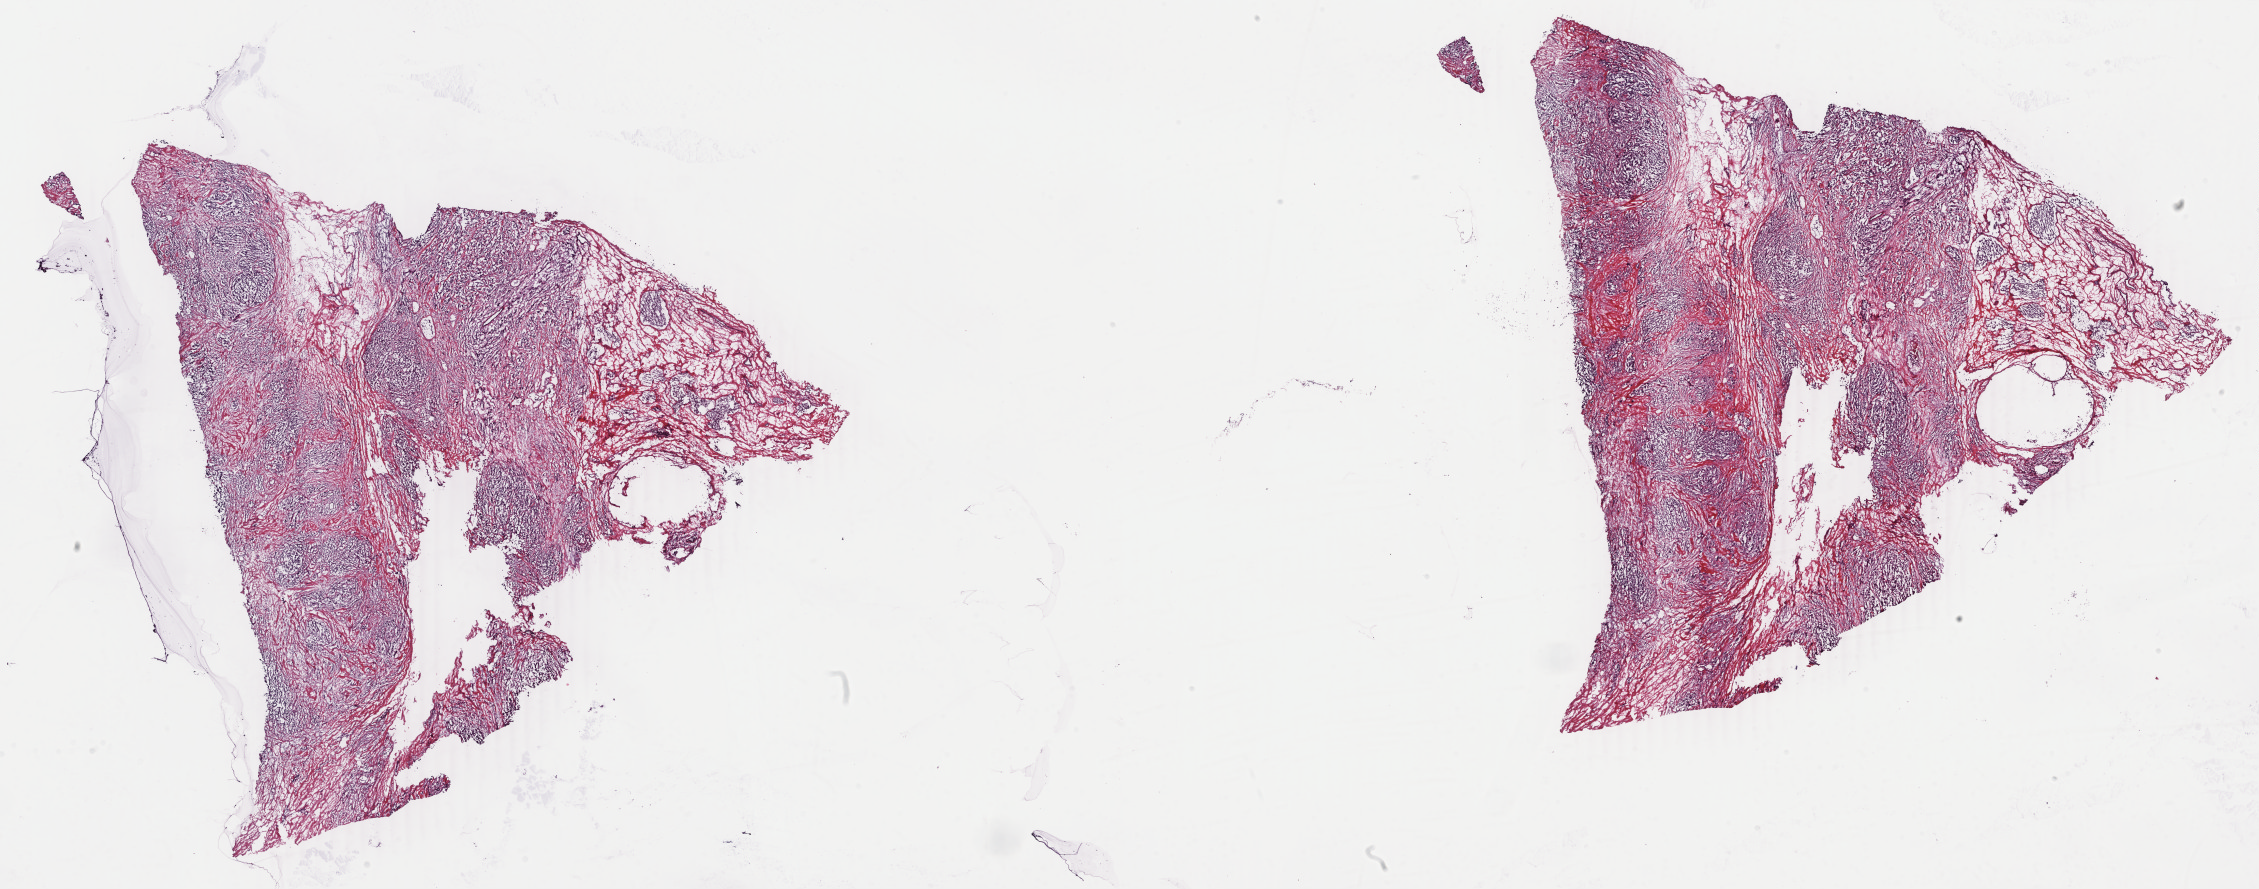
Whole-slide histology image, Hematoxylin and eosin (H&E) stained — a low-resolution overview of the entire scanned area, about 35.9 x 14.1 mm (acquisition: 40x scan). Frozen section from the top of the tissue portion. Breast, primary tumour sample. Patient: female, age at initial diagnosis 72 years. Pathologist review of this section (percent, as recorded): tumour cells 75%, tumour nuclei 85%, normal cells 0%, stromal cells 25%, necrosis 0%. Infiltration values recorded for this section: lymphocyte infiltration 0%, monocyte infiltration 0%, neutrophil infiltration 0%.
• pathologic diagnosis: Lobular carcinoma, NOS
• laterality: right
• lymph nodes positive (case pathology): 5 of 31 examined
• AJCC pathologic stage: IIIA (6th edition)